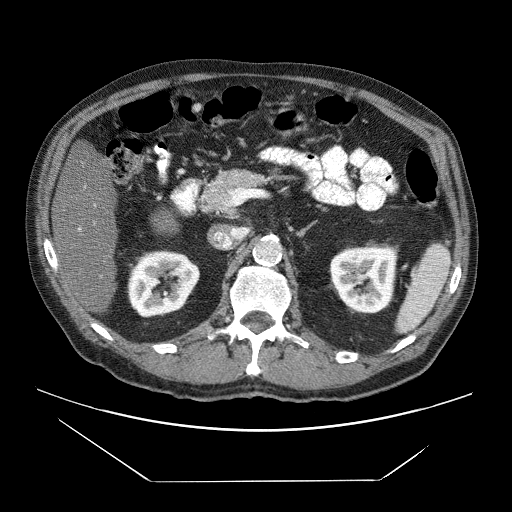
Contrast-enhanced abdominal CT (liver protocol), one axial slice; slice 23 of 83 in the series (ordered by position); 120 kVp; soft-tissue window (W 400 / L 40 HU); 2.5 mm slice thickness; 512 × 512 image matrix, field of view 420 × 420 mm. From the clinical record (not read from this slice): diagnosis: hepatocellular carcinoma (patient treated with transarterial chemoembolisation; whether this scan precedes or follows treatment is not stated here); TNM stage (as recorded): Stage-IVB; Child-Pugh class: B.
Annotated regions visible in this slice (semi-automatic segmentation, software-assisted and operator-edited):
- liver parenchyma outside the tumour (the mass and vessels are separate outlines, so this box may not span the whole liver): box from (x=52, y=152) to (x=118, y=312) px